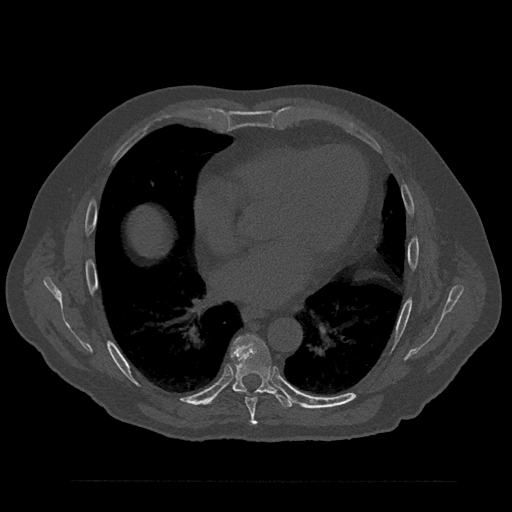
CT including the spine, one axial slice. Position 478 of 797 along the scan axis. Reconstruction kernel Br40s/3. Bone window (W 1800 / L 400 HU). 512 × 512 image matrix, field of view 430 × 430 mm. Male patient, age 61 years. Case-level facts recorded for this patient, not image findings: primary cancer: prostate.
Annotated regions visible in this slice (semi-automatically segmented with operator editing):
- T7 vertebra: box from (x=241, y=391) to (x=259, y=426) px
- T8 vertebra: (x=231, y=335)–(x=295, y=408)